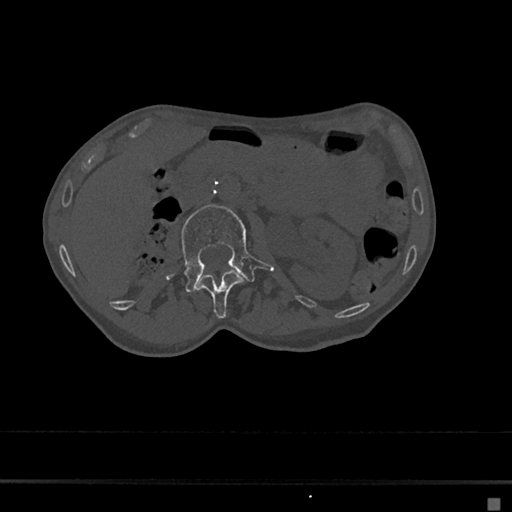
CT including the spine, one axial slice; slice 32 of 797 in the series (ordered by position); bone window (W 1800 / L 400 HU); 0.5 mm slice thickness; 512 × 512 image matrix, field of view 360 × 360 mm. Patient: female, 68 years. Case-level facts recorded for this patient, not image findings: primary cancer: renal.
Structures marked on this image (semi-automatically segmented with operator editing):
- L1 vertebra: bounding box (x1, y1, x2, y2) in pixels: (196, 270, 244, 319)
- L2 vertebra: (167, 204, 273, 292)